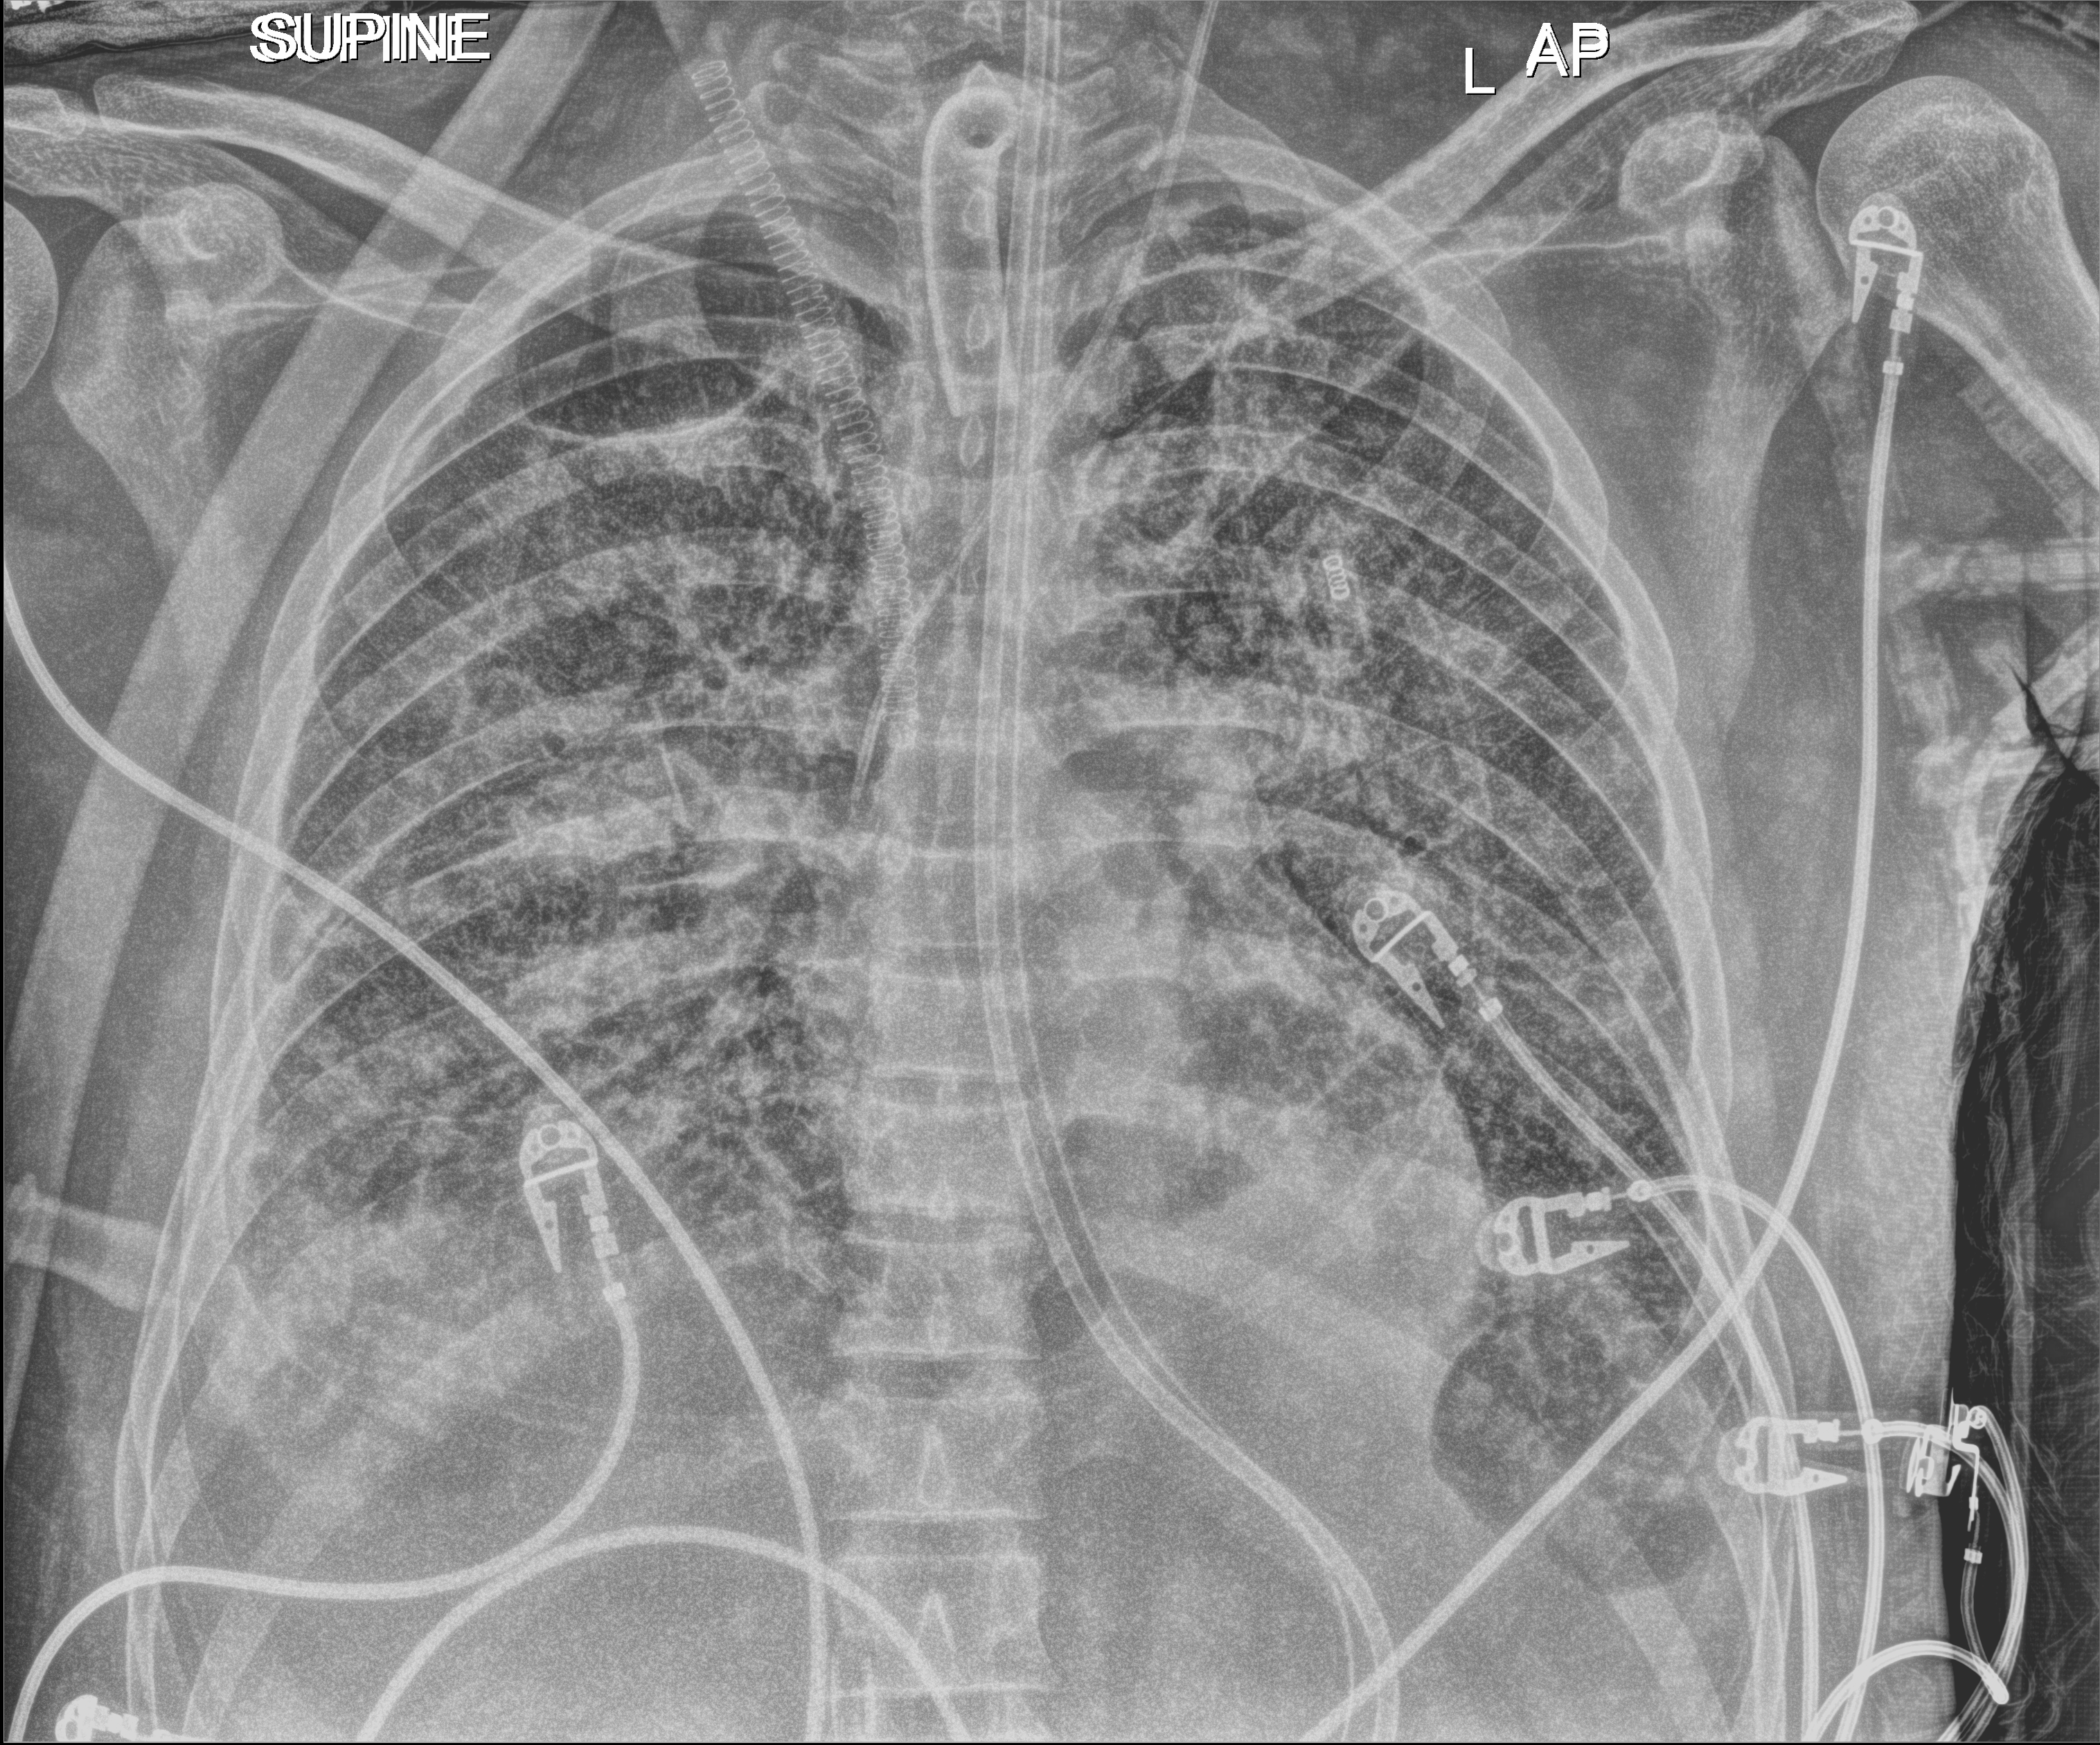
Bedside chest radiograph (digital radiography), anteroposterior (AP) projection. Adult patient hospitalised with COVID-19, age 18–59 years.
Hospital-stay facts (about this admission, not read from this image; timing relative to this image not recorded):
- admitted to intensive care during this hospital stay: yes
- hypertension (admission record): no
- mechanically ventilated during this hospital stay: yes